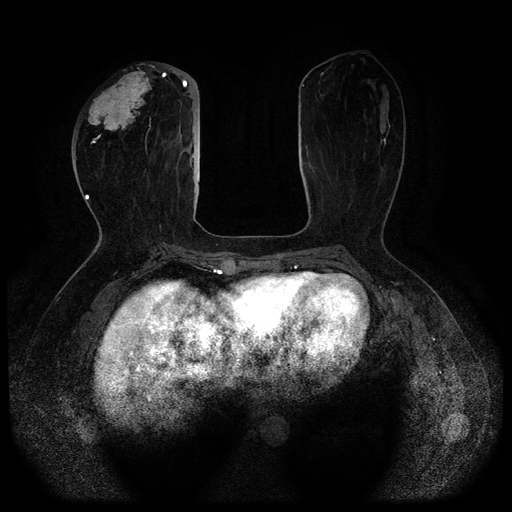
Breast MRI (dynamic contrast-enhanced, multi-phase), one axial slice; dynamic contrast-enhanced series, time point 2 of 5 at this slice position (early post-contrast); 1.5 T; TE 2.6 ms, TR 5.3 ms; 2 mm slice thickness; 512 × 512 image matrix. Patient: female, 51 years.
Structures marked on this image (semi-automatic segmentation, software-assisted and operator-edited):
- breast lesion (labelled 'tumour' in the annotation; benign lesions carry a separate 'benign' label): bounding box [x1, y1, x2, y2] px = [87, 67, 152, 144]